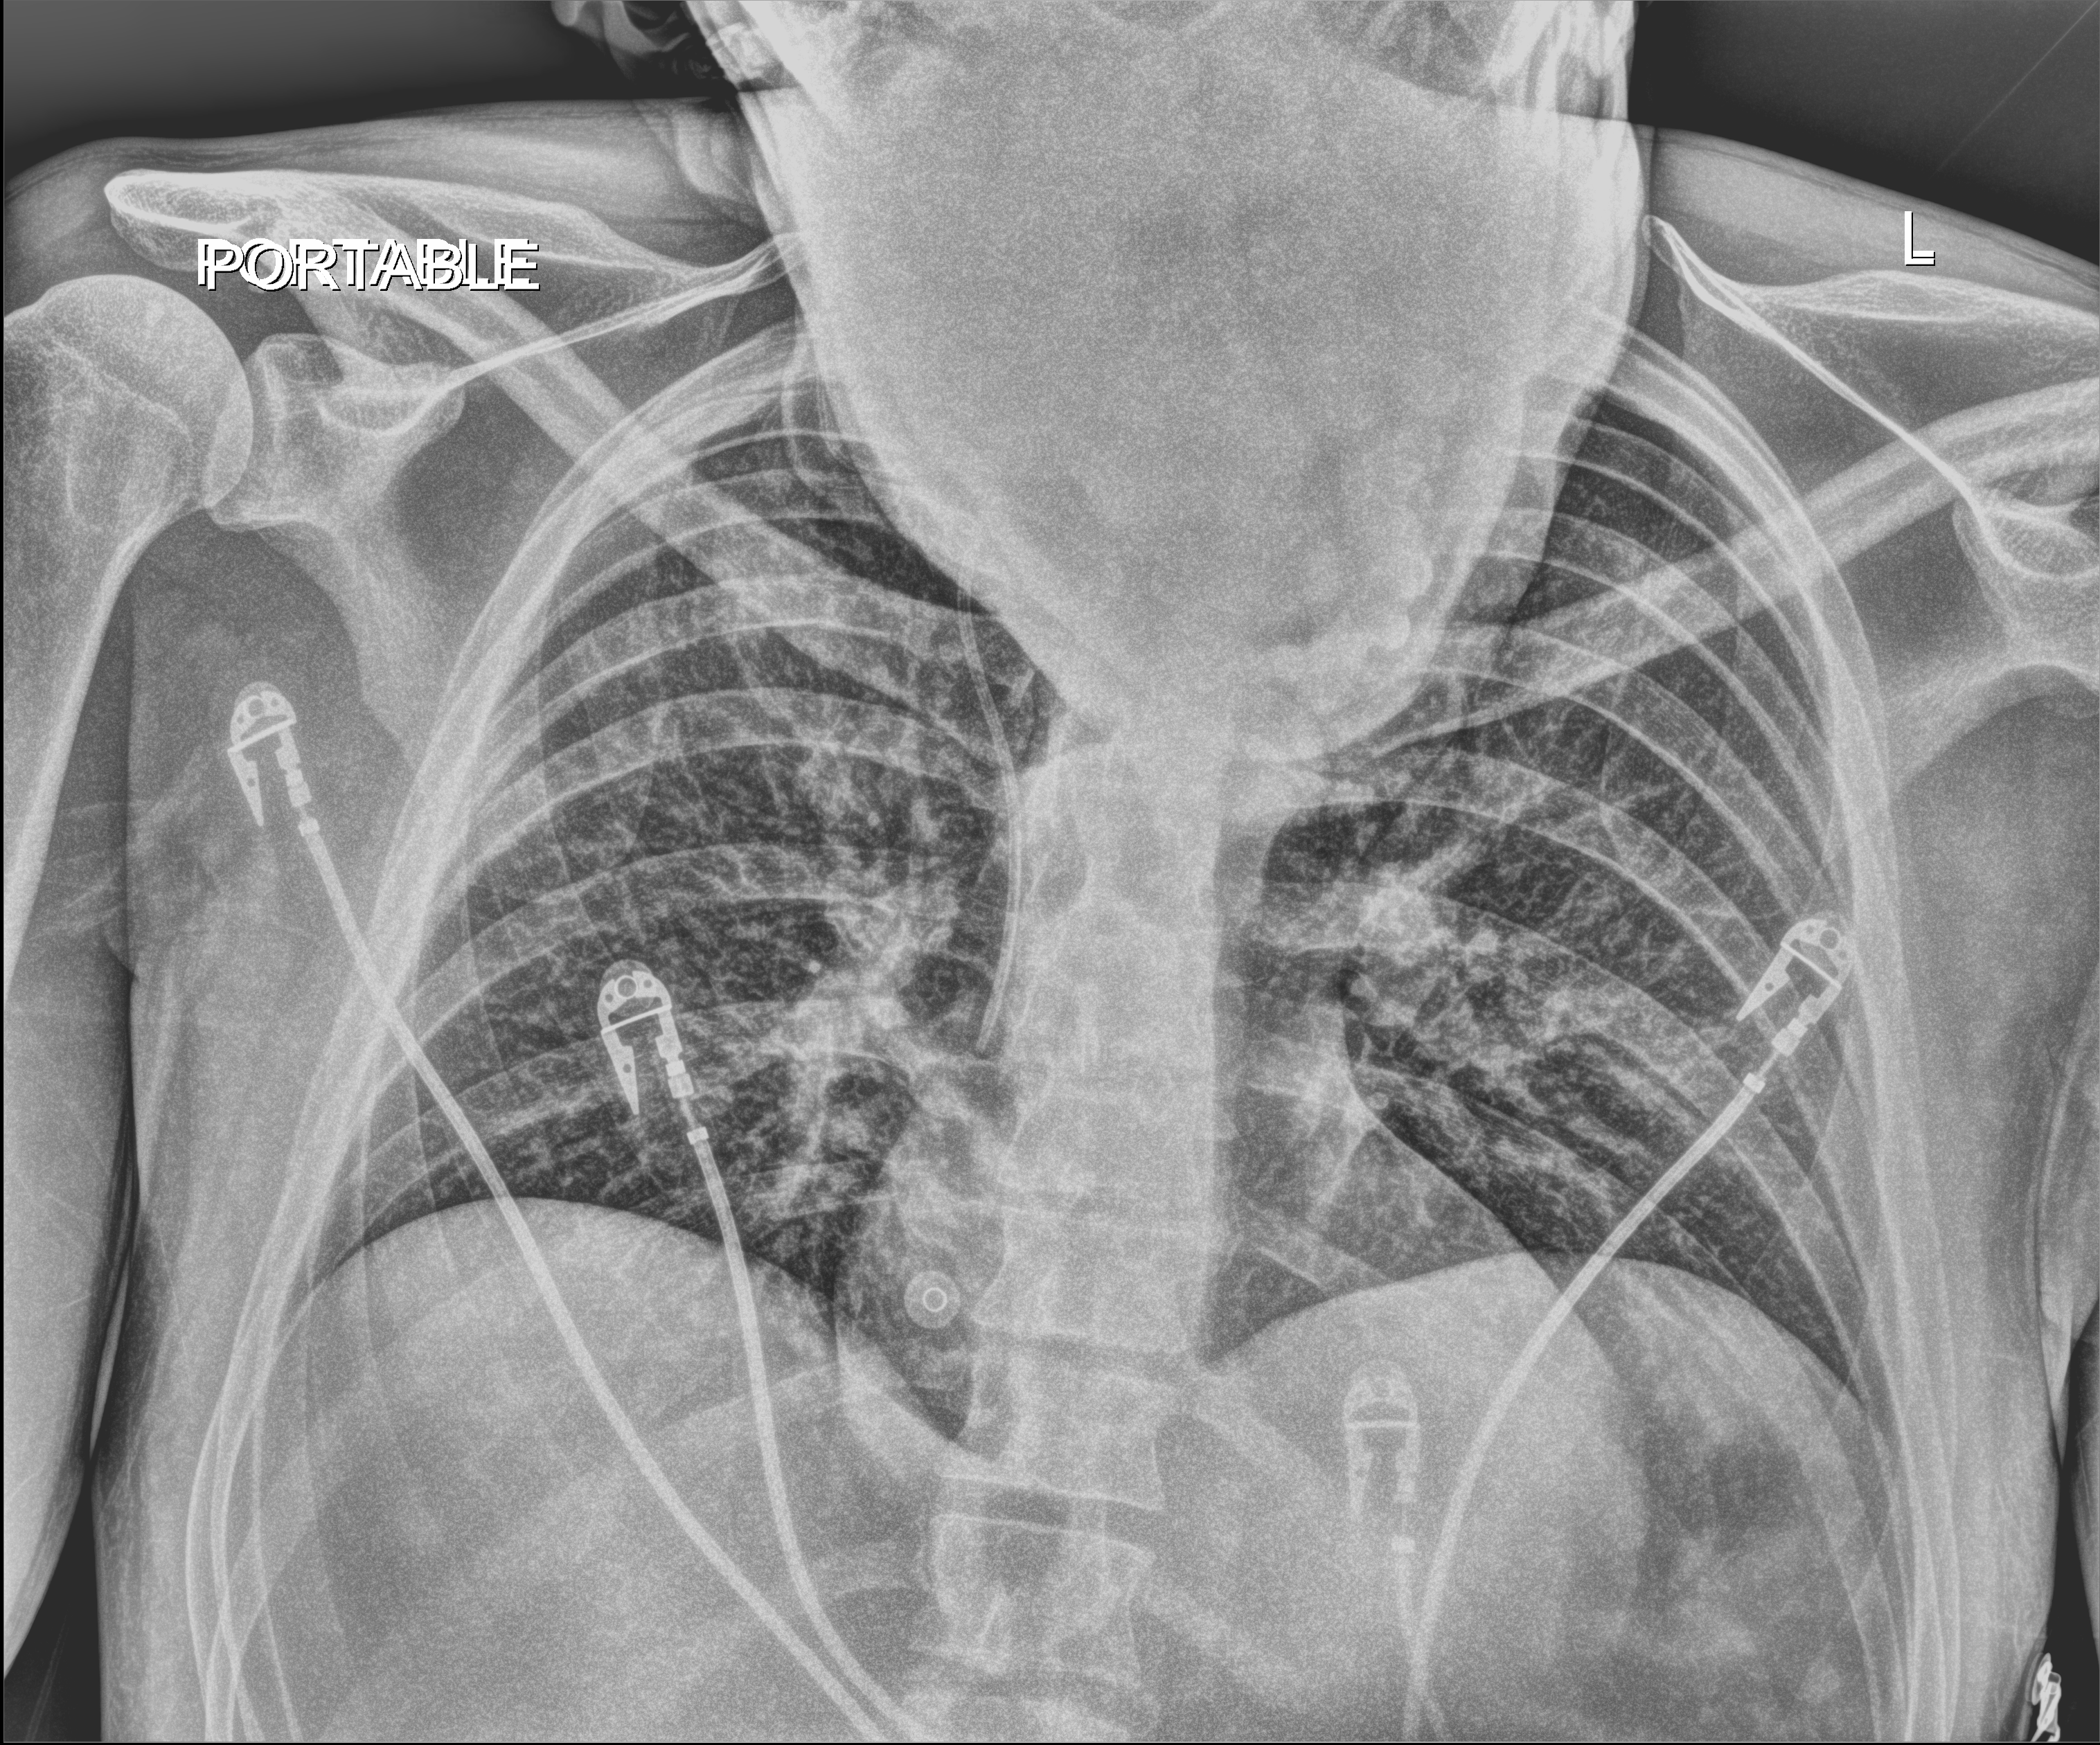
Portable chest radiograph, anteroposterior (AP) projection. Male patient hospitalised with COVID-19, age 18–59 years.
Admission-level facts for this patient (not findings on this image; timing relative to this image not recorded):
- mechanically ventilated during this hospital stay: yes
- admitted to intensive care during this hospital stay: no